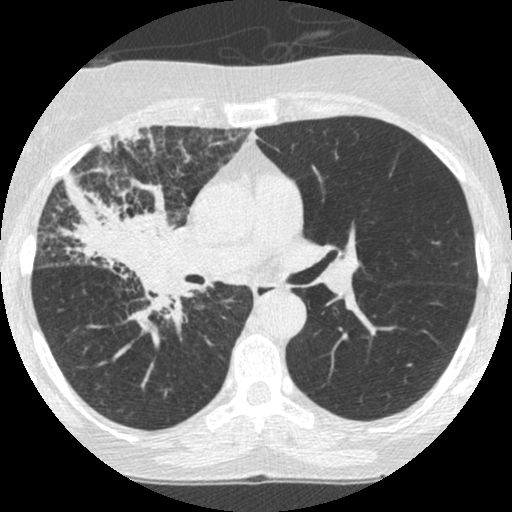
Low-dose screening chest CT, one axial slice. Lung window (W 1500 / L -600 HU). 1.25 mm slice thickness. 512 × 512 image matrix, field of view 294 × 294 mm.
Structures marked on this image (outlined manually by an expert reader):
- lesion 2 (tumor, hilum of right lung): box from (x=50, y=168) to (x=188, y=351) px
- lesion 3 (tumor, upper lobe of right lung): (x=100, y=127)–(x=167, y=161)